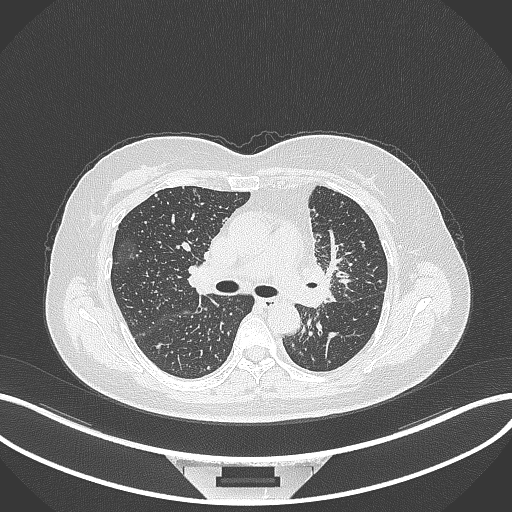
Chest CT, one axial slice. Slice 206 of 348 in the series (ordered by position). Reconstruction kernel B70f. Lung window (W 1500 / L -600 HU). 1 mm slice thickness. 512 × 512 image matrix, field of view 400 × 400 mm. Female patient, age 49 years. From the clinical record (not read from this slice): clinical TNM (as recorded): T1c N0 M1.
Annotated regions visible in this slice (rectangle marked by the reading radiologist):
- lung tumour (recorded histology: adenocarcinoma): box from (x=294, y=254) to (x=336, y=311) px